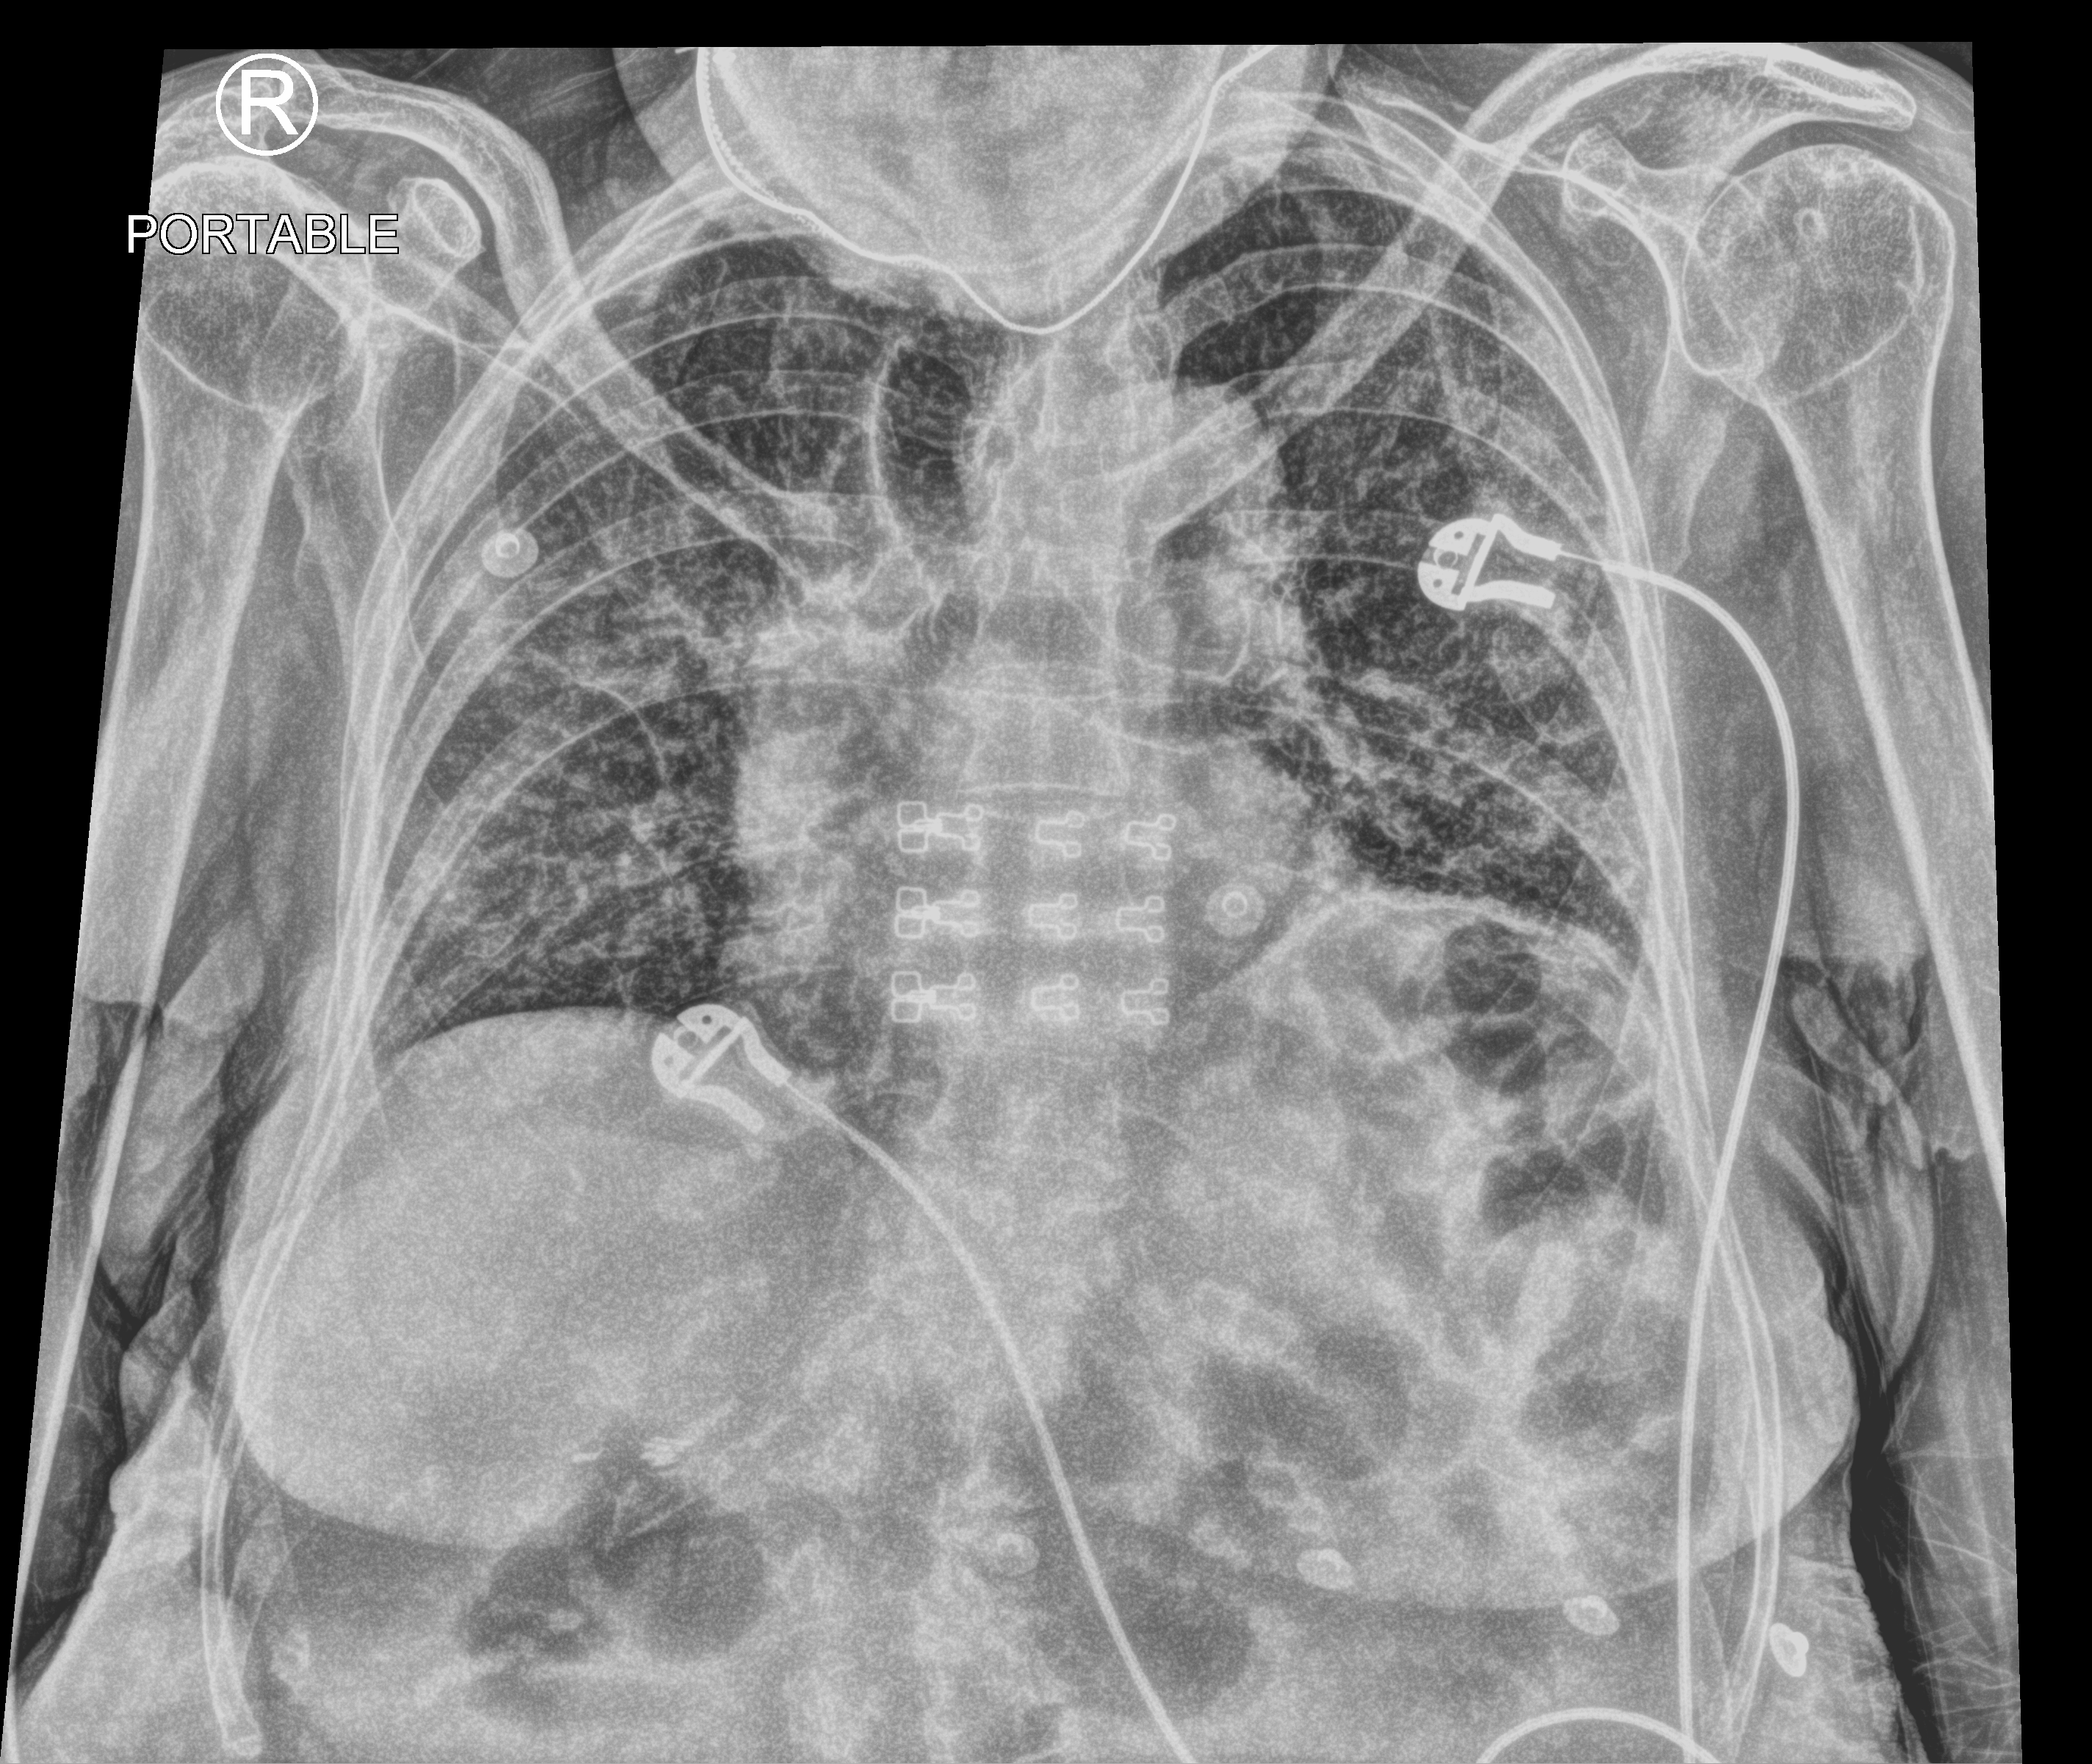
Portable chest radiograph. Female patient hospitalised with COVID-19, age 75–90 years.
Admission-level facts for this patient (not findings on this image; timing relative to this image not recorded):
- admitted to intensive care during this hospital stay: no